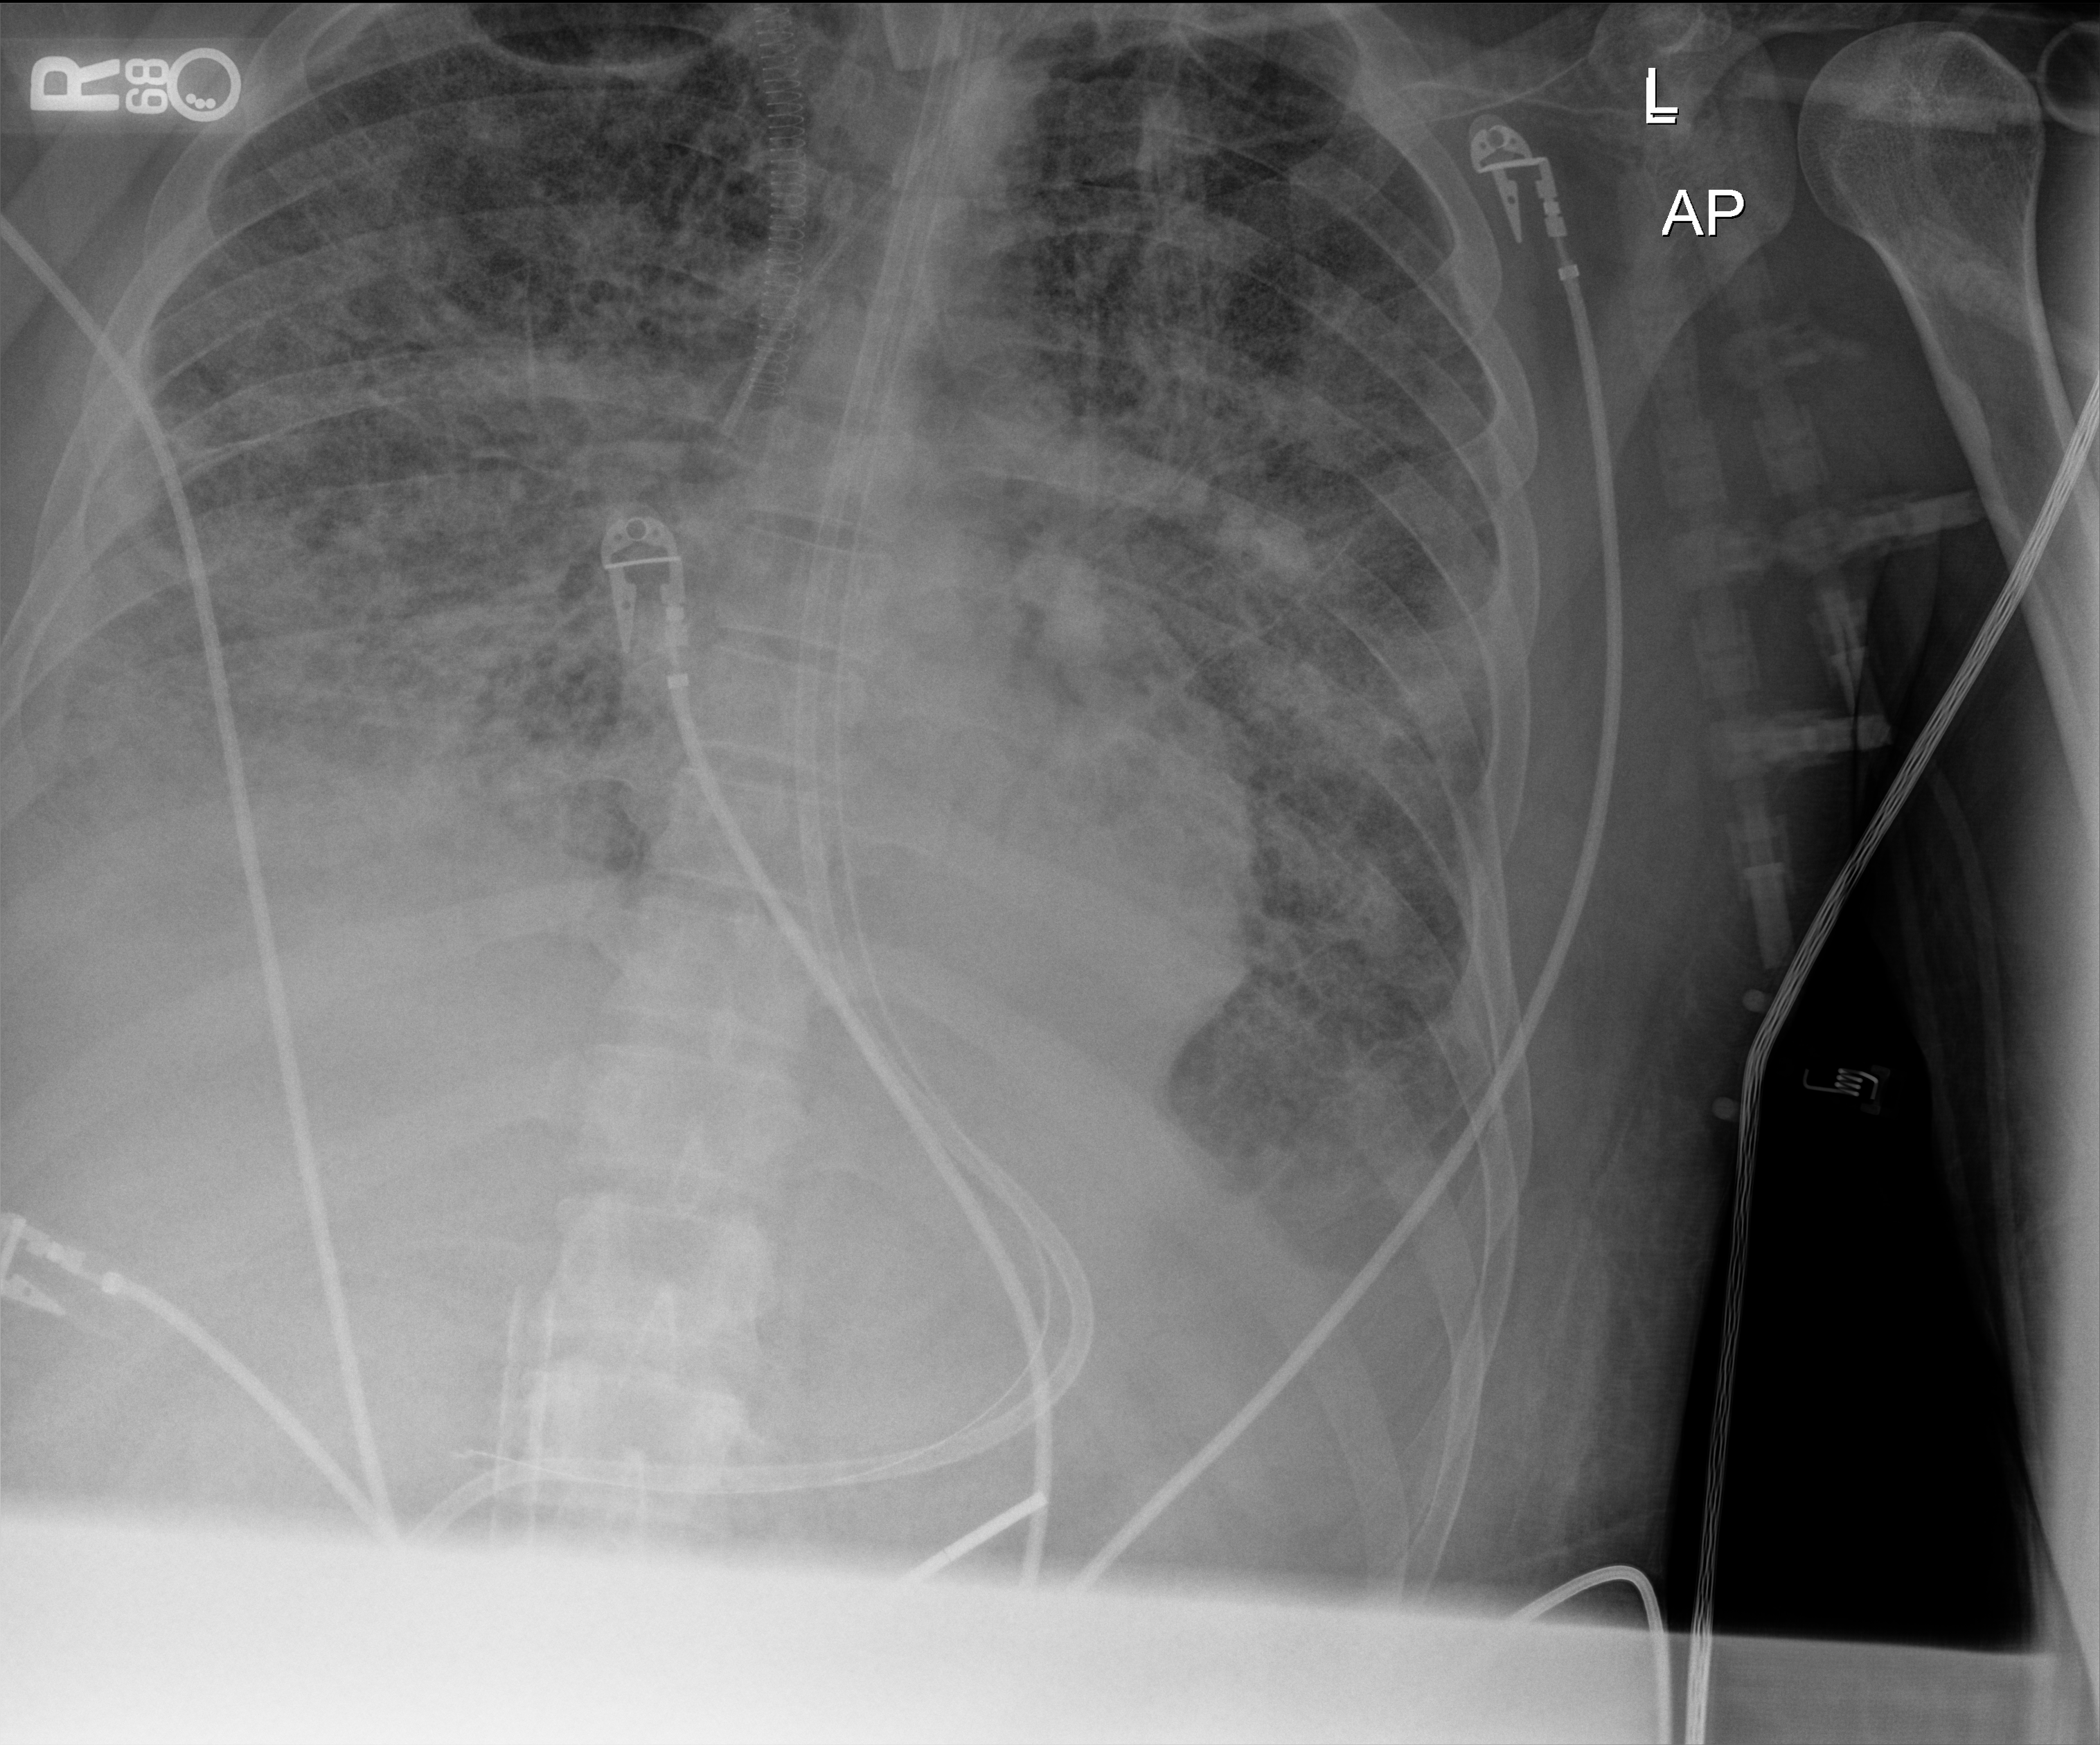
Chest radiograph; anteroposterior (AP) projection. Adult patient hospitalised with COVID-19, age 18–59 years.
From the hospital-stay record, not from the radiograph (when in the stay this image was taken is not recorded): smoking status (admission record): never; length of hospital stay: 60 days; mechanically ventilated during this hospital stay: yes.